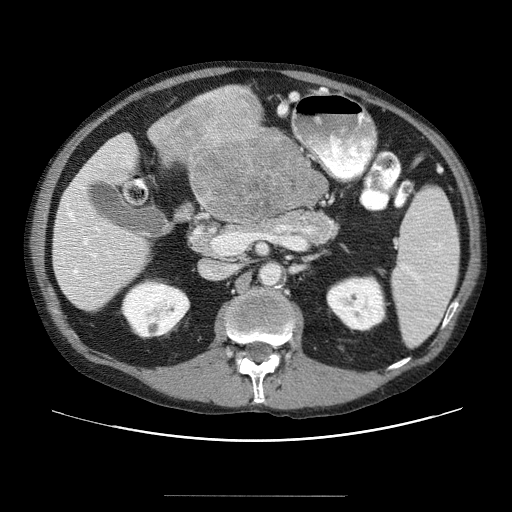
Contrast-enhanced abdominal CT (liver protocol), one axial slice. Slice 14 of 69 in the series (ordered by position). Soft-tissue window (W 400 / L 40 HU). 2.5 mm slice thickness. 512 × 512 image matrix. From the clinical record (not read from this slice): diagnosis: hepatocellular carcinoma (patient treated with transarterial chemoembolisation; whether this scan precedes or follows treatment is not stated here); TNM stage (as recorded): Stage-IVB.
Outlined on this slice (semi-automatic segmentation, software-assisted and operator-edited):
- liver parenchyma outside the tumour (the mass and vessels are separate outlines, so this box may not span the whole liver): box from (x=52, y=110) to (x=320, y=306) px
- mass: (x=151, y=89)–(x=312, y=225)
- liver vessels: (x=57, y=159)–(x=127, y=301)